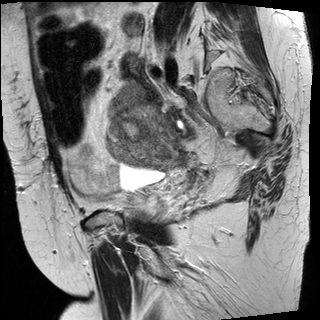
Pelvic MRI for cervical cancer, one sagittal slice. Position 22 of 30 along the scan axis. T2-weighted. 1.5 T. TE 89 ms, TR 3810 ms. 320 × 320 image matrix. Patient: female, 62 years.
Structures marked on this image (manually delineated by an expert):
- uterus and cervix: box from (x=106, y=107) to (x=190, y=170) px